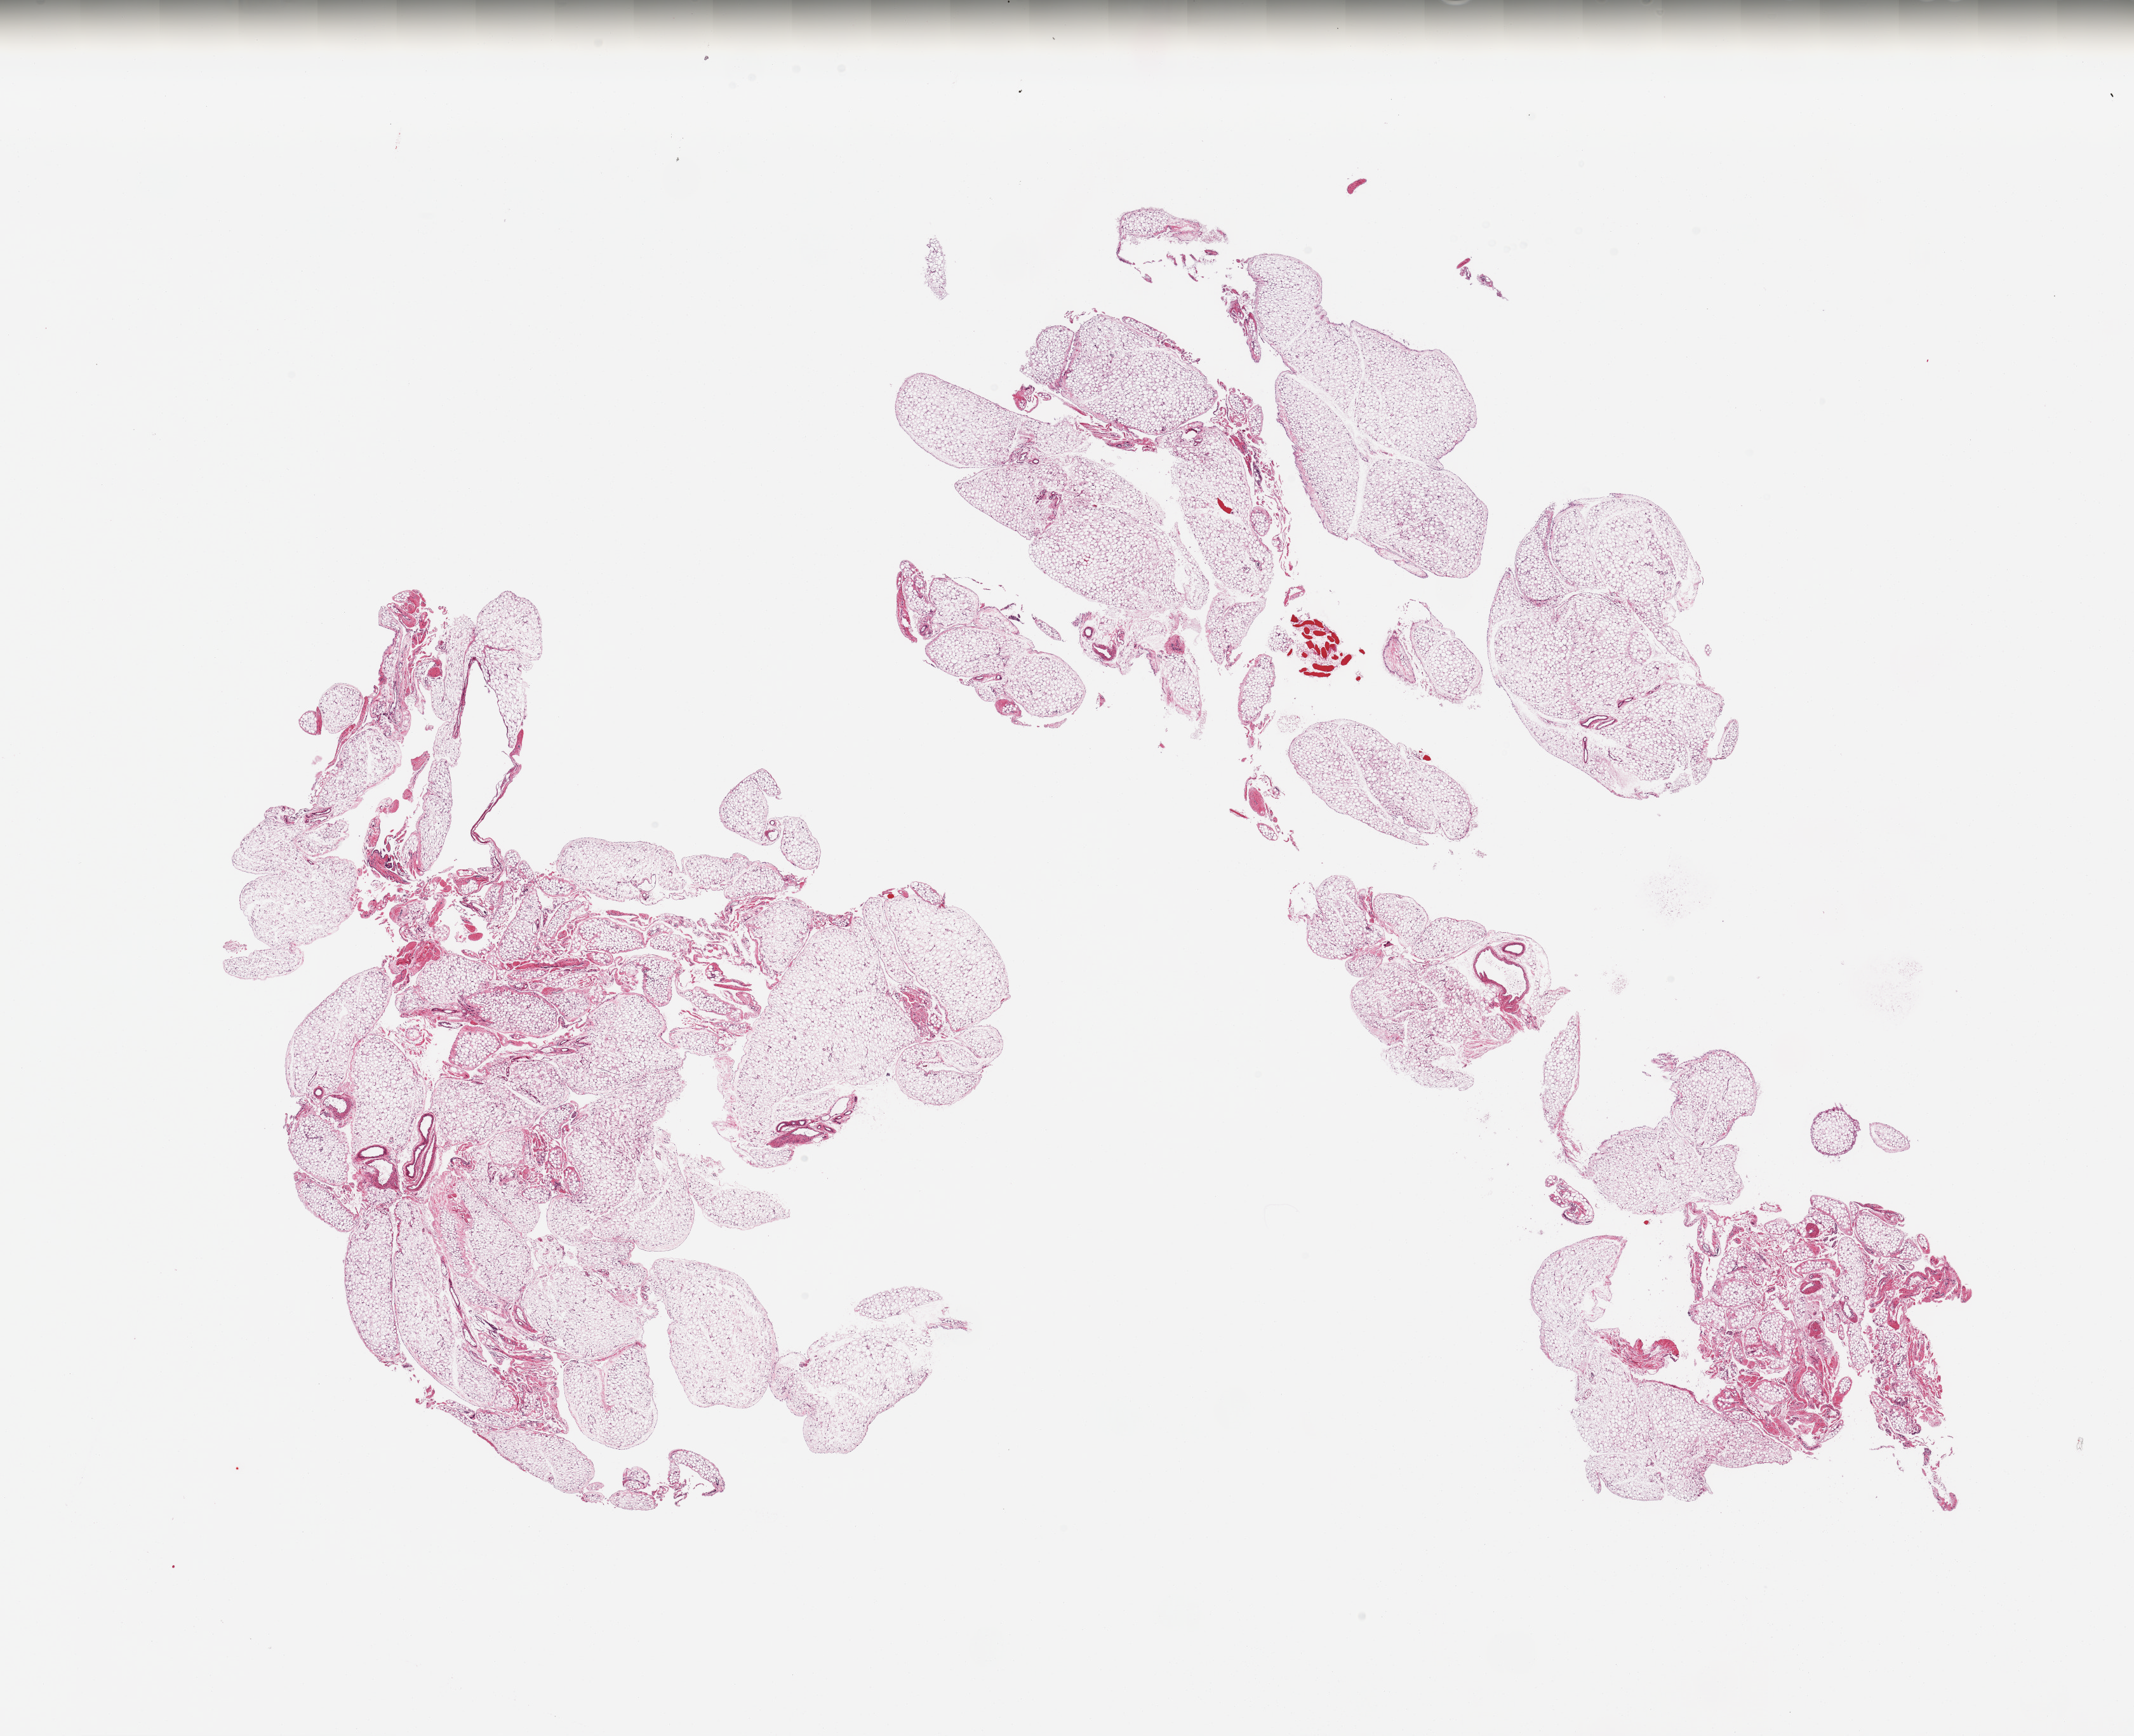
Digitized H&E-stained section, shown as a low-resolution overview of the whole scanned area (about 26.6 x 21.6 mm, acquisition: 20x scan); PAXgene-fixed paraffin-embedded (PFPE) section; sampled site (target tissue): omentum; donor tissue sample.
Pathologist's review note for this sample: 2 pieces, 5-10% fascia/mesothelium/vascular elements.